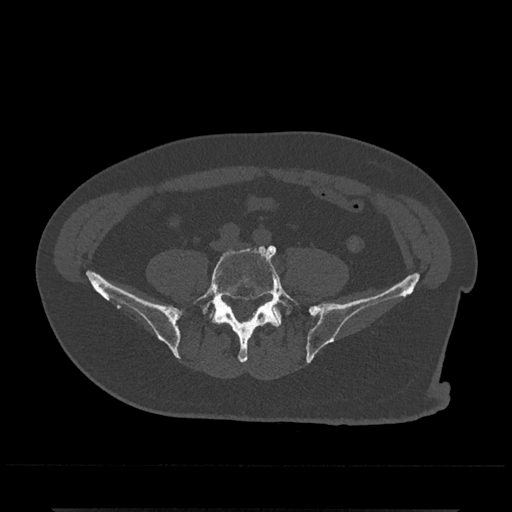
CT including the spine, one axial slice; slice 84 of 797 in the series (ordered by position); reconstruction kernel Br40s/3; 120 kVp; bone window (W 1800 / L 400 HU); 0.5 mm slice thickness; 512 × 512 image matrix, field of view 393 × 393 mm. Male patient, age 67 years. Case-level facts recorded for this patient, not image findings: primary cancer: prostate.
Outlined on this slice (semi-automatic segmentation, software-assisted and operator-edited):
- L5 vertebra: bounding box (x1, y1, x2, y2) in pixels: (192, 245, 300, 363)